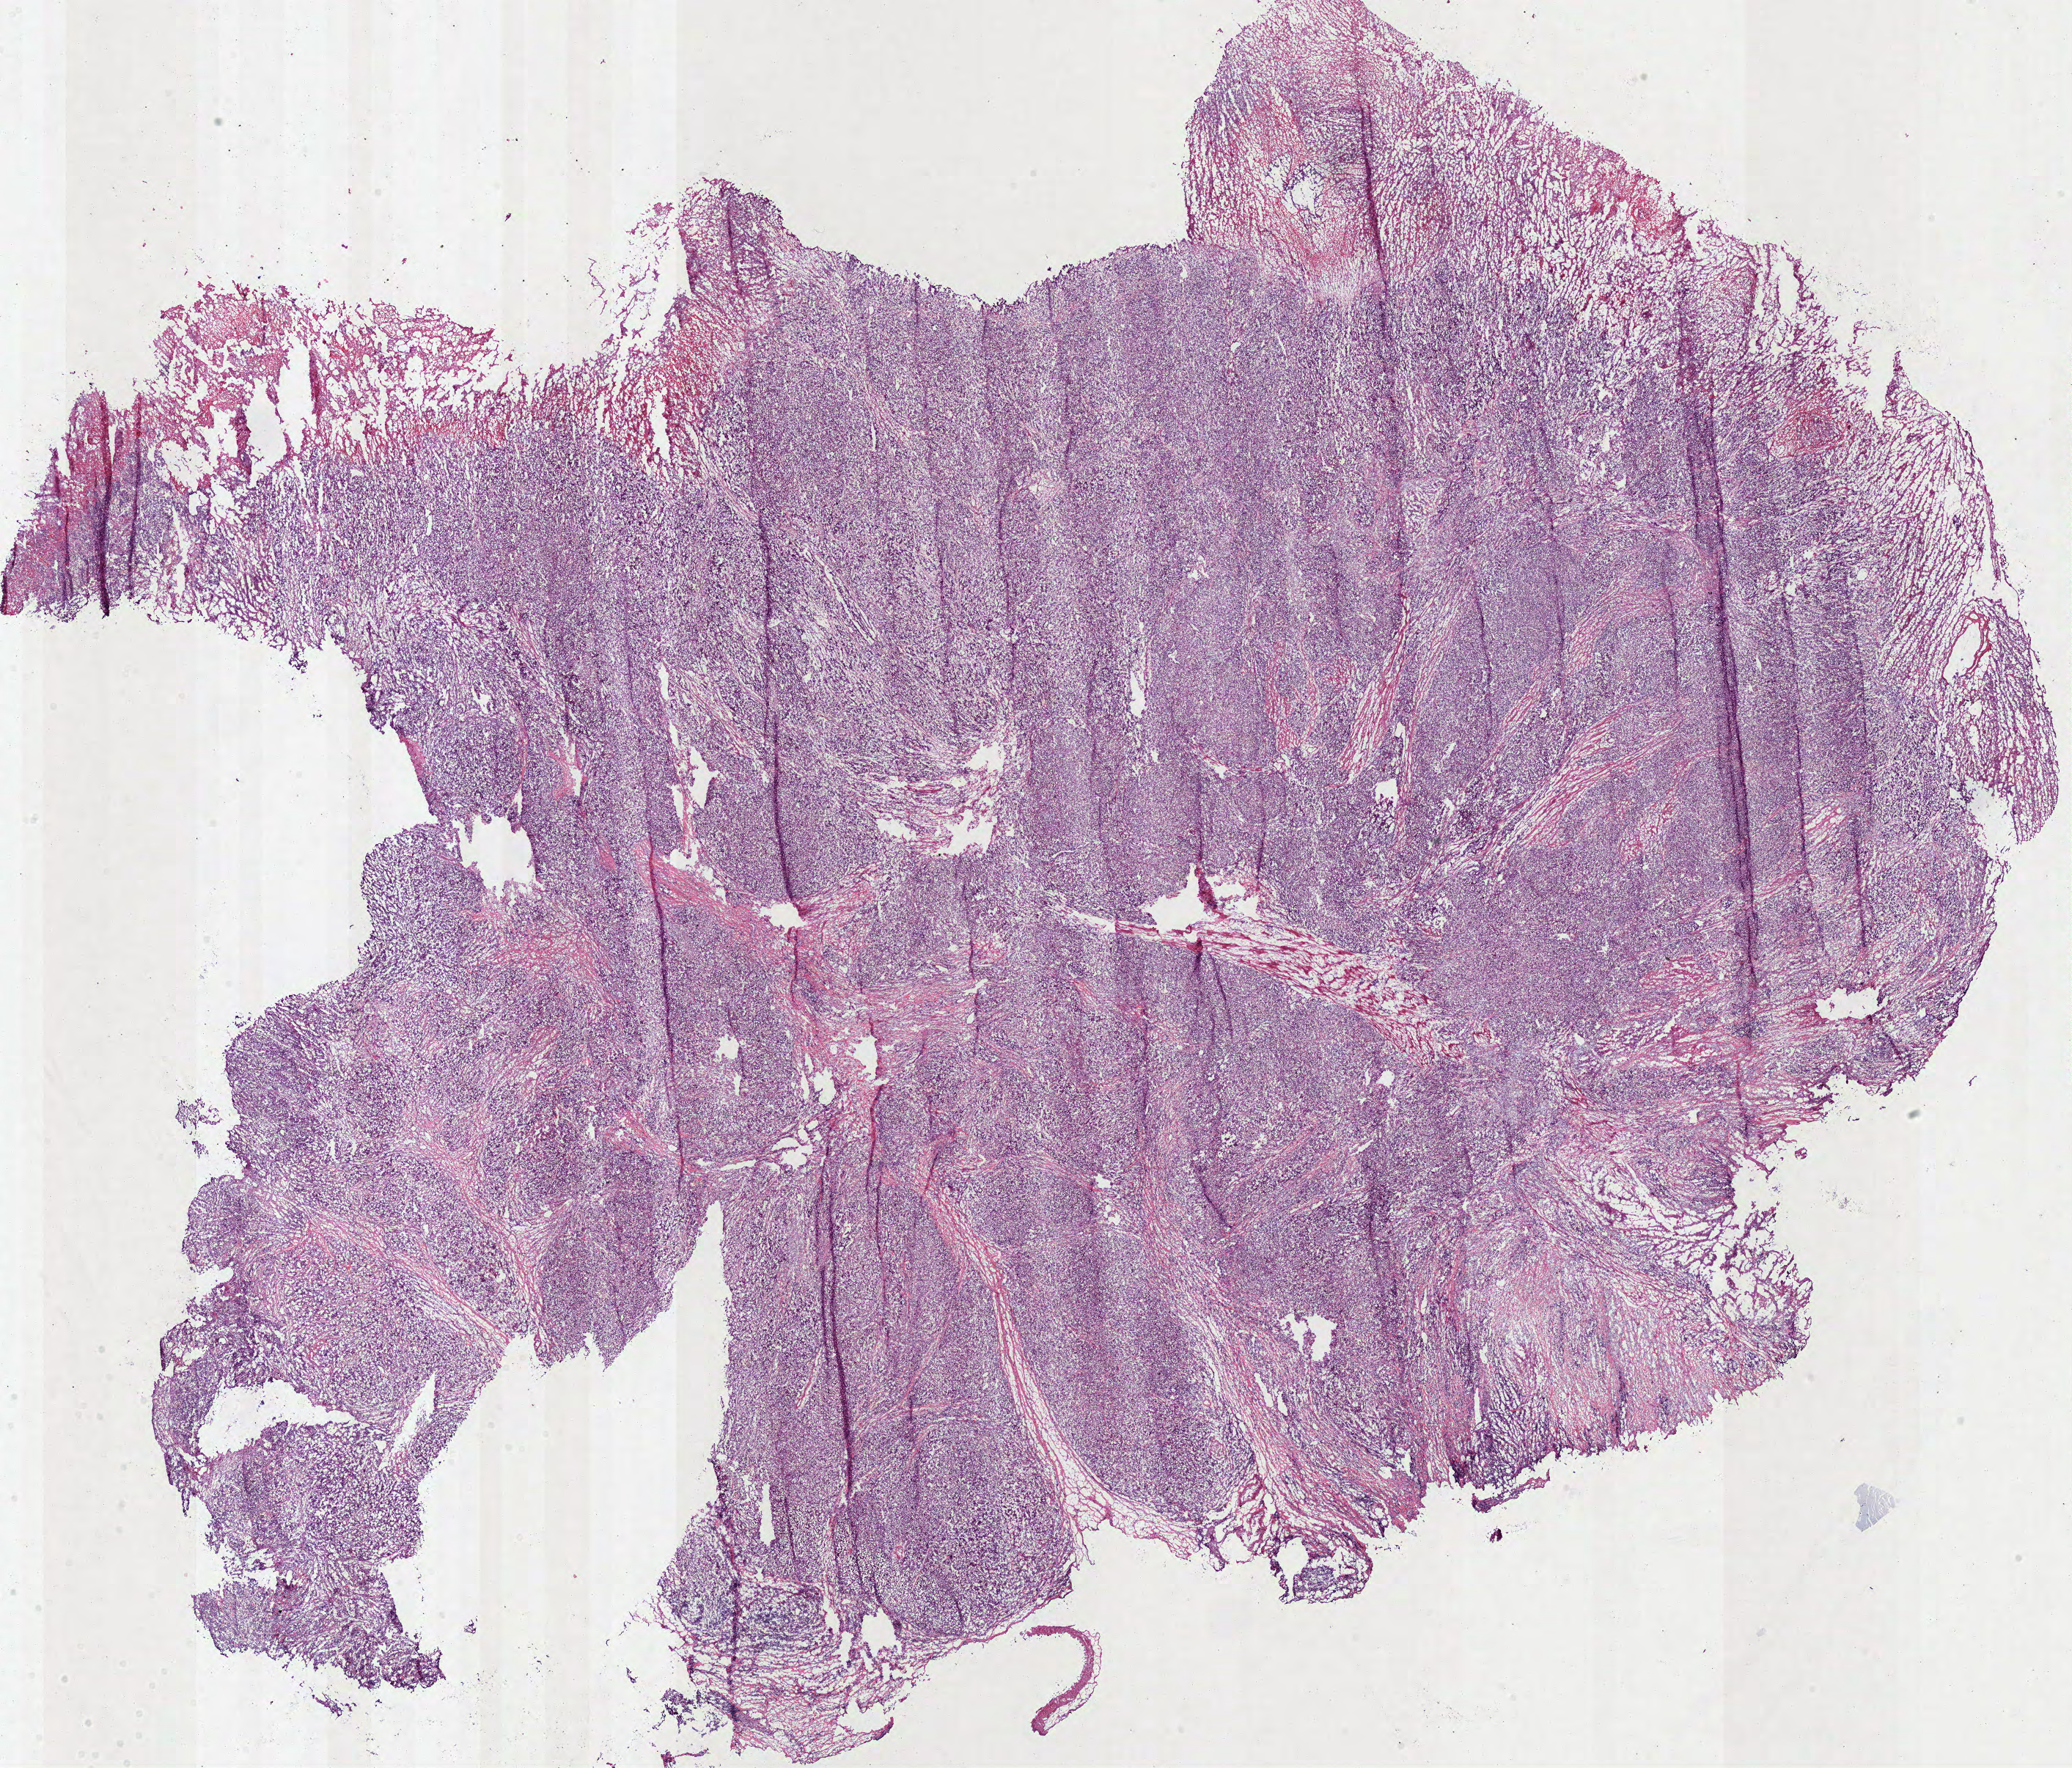
Whole-slide histology image, H&E, shown as a low-resolution overview of the whole scanned area (about 22.3 x 19.0 mm), frozen section, sample: primary tumour, stomach. Female, age 64 years at initial diagnosis.
Pathologic diagnosis: Adenocarcinoma, NOS (cardia, NOS).